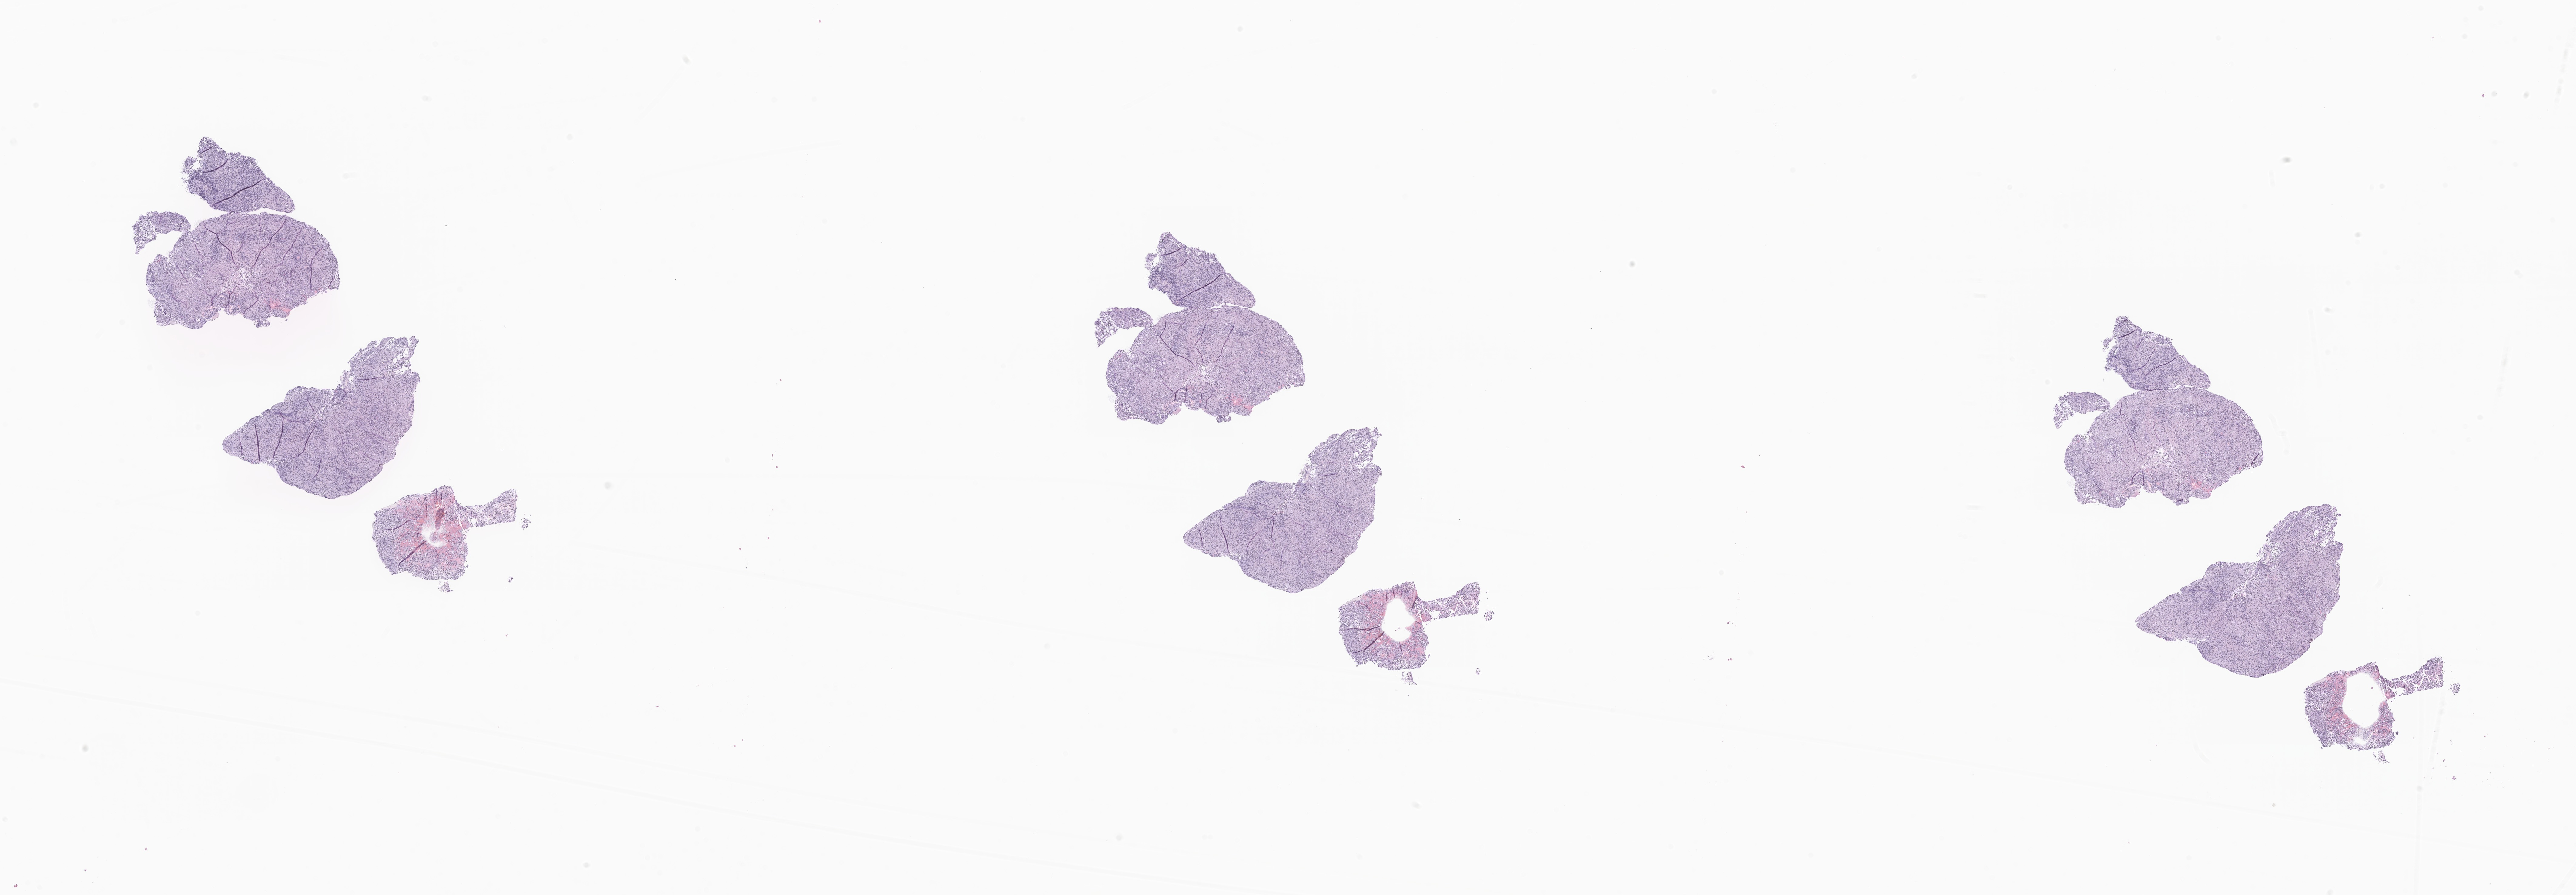
Whole-slide image, hematoxylin and eosin (H&E) stain of tumor tissue from the brain, a low-resolution overview of the entire scanned area, about 35.8 x 12.4 mm; formalin-fixed, paraffin-embedded (FFPE) tissue. Patient male; age 197 months (16 years 5 months).
Diagnosis: Germinoma.